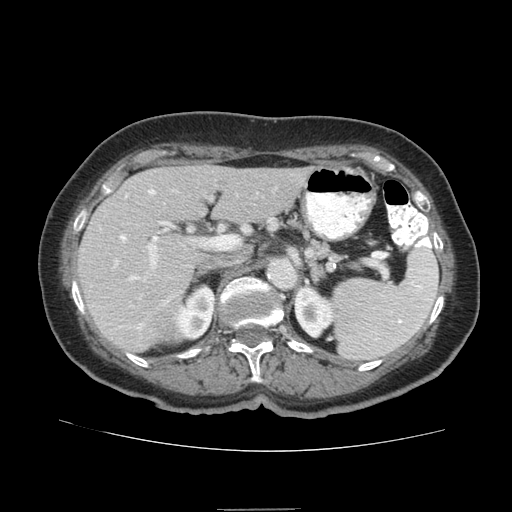
Contrast-enhanced abdominal CT (liver protocol), one axial slice; slice 45 of 95 in the series (ordered by position); reconstruction kernel STANDARD; 140 kVp; soft-tissue window (W 400 / L 40 HU); 2.5 mm slice thickness; 512 × 512 image matrix, field of view 360 × 360 mm. From the clinical record (not read from this slice): diagnosis: hepatocellular carcinoma (patient treated with transarterial chemoembolisation; whether this scan precedes or follows treatment is not stated here); TNM stage (as recorded): Stage-IVA; Child-Pugh class: B; tumour differentiation: moderately differentiated.
Outlined on this slice (semi-automatically segmented with operator editing):
- liver parenchyma outside the tumour (the mass and vessels are separate outlines, so this box may not span the whole liver): bounding box (x1, y1, x2, y2) in pixels: (76, 164, 314, 351)
- mass: (151, 305, 175, 337)
- liver vessels: (116, 190, 222, 329)